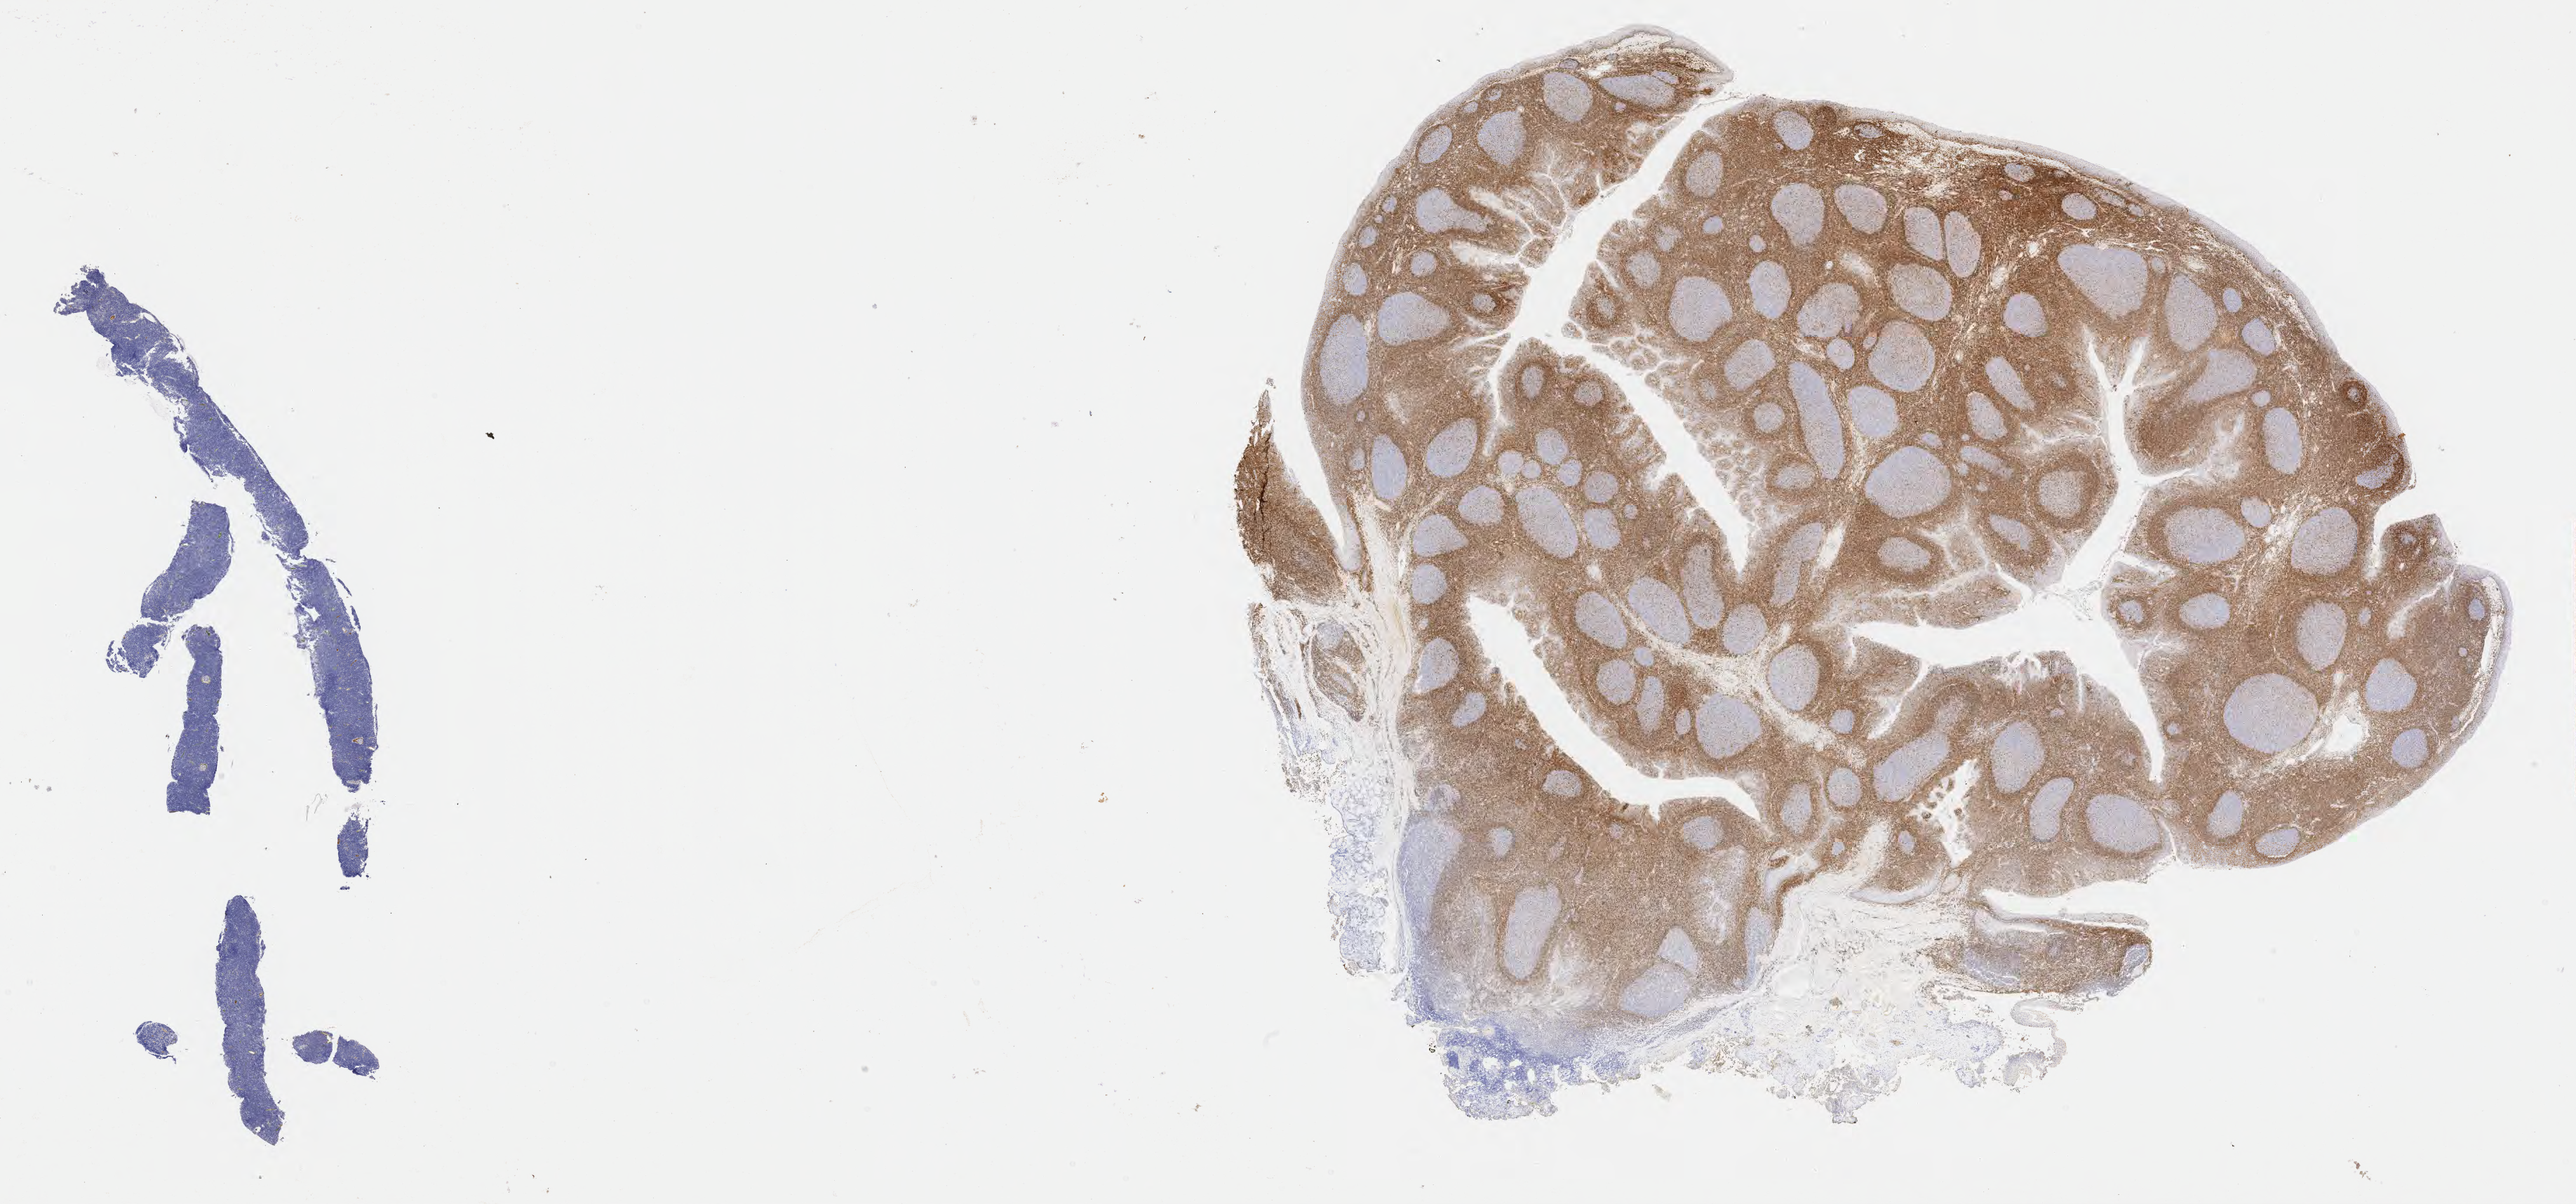
Immunohistochemistry (IHC) whole-slide image stained for BCL2 — whole scanned area (about 29.7 x 13.9 mm) shown as a low-resolution overview, specimen: tumor tissue. Patient: male, age at initial diagnosis 8 years.
* histologic diagnosis: Burkitt lymphoma, NOS